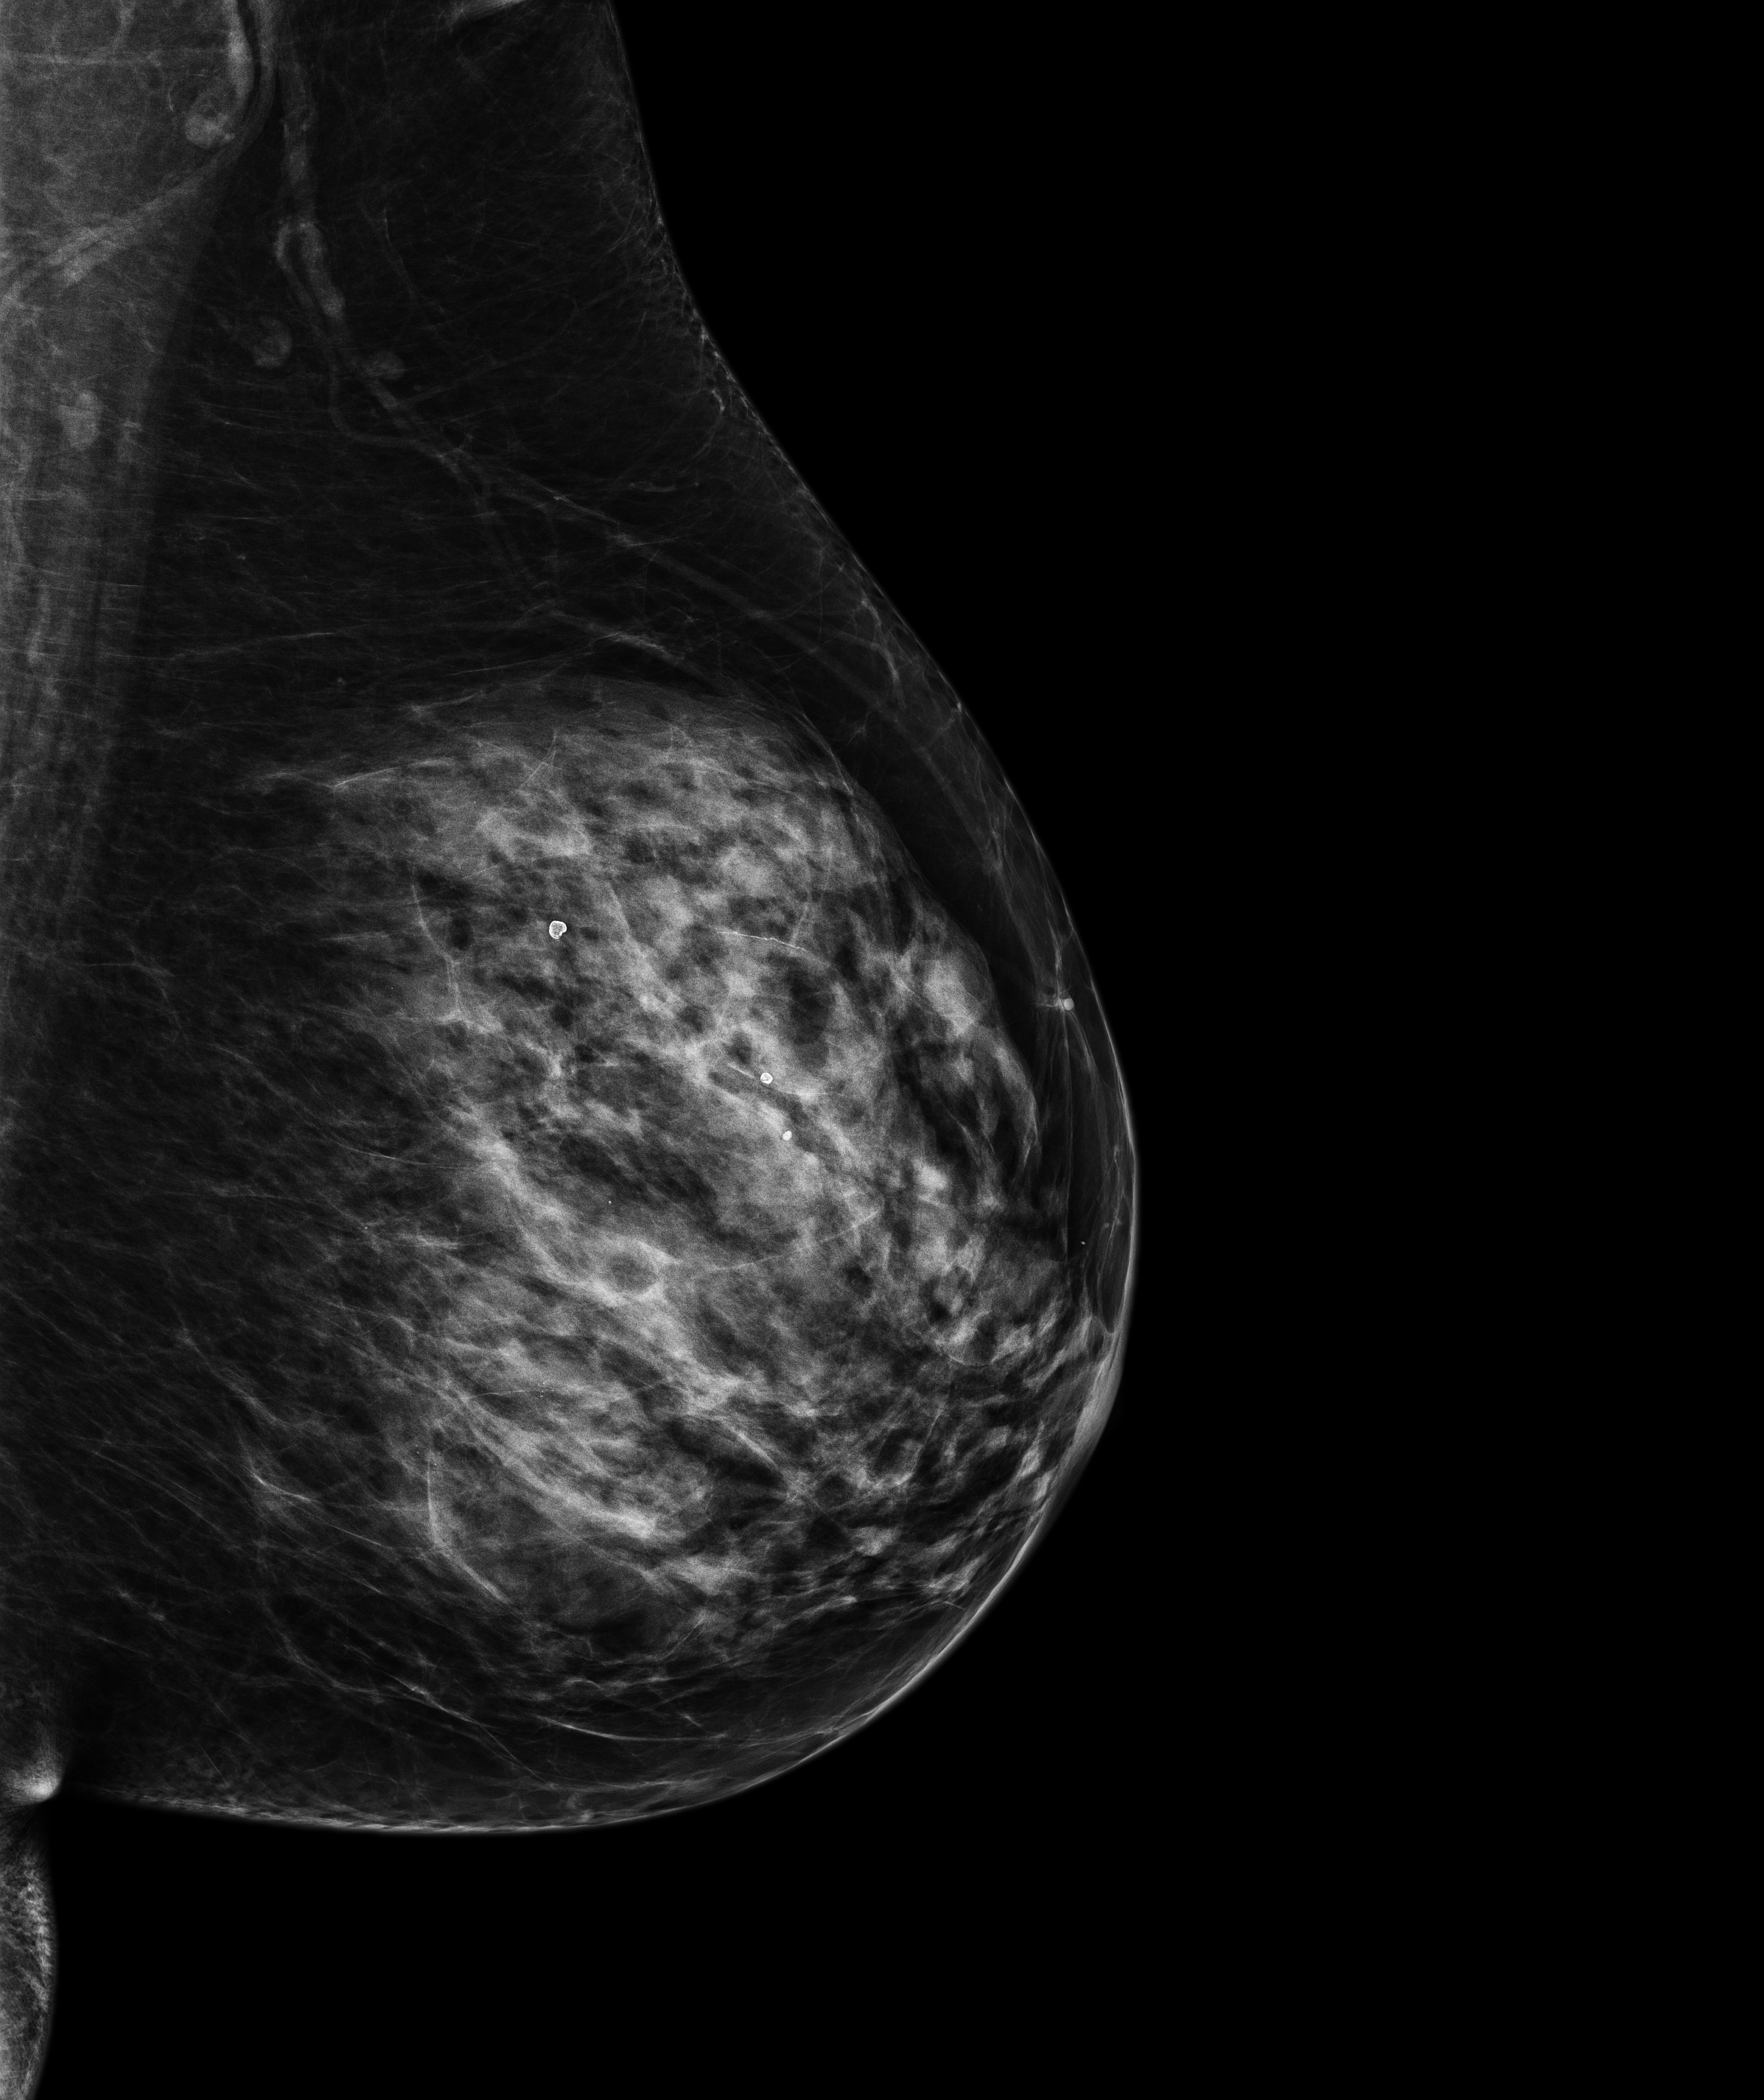
Screening examination. Female patient, age 66 years.
Image type: full-field digital mammogram. Breast: left. Projection: medio-lateral oblique projection.